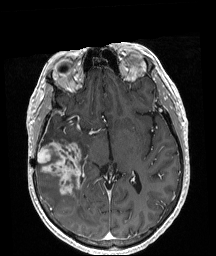
Brain MRI from a brain-tumour surgery series, one axial slice. Slice 109 of 208 in the series (ordered by position). T1-weighted post-contrast. 1 mm slice thickness. 216 × 256 image matrix, field of view 211 × 250 mm. From the clinical record (not read from this slice): histopathology: Astrocytoma; WHO grade: 4; IDH mutation: yes; tumour location: Right Temporal.
Outlined on this slice (expert manual segmentation):
- tumour: bounding box [x1, y1, x2, y2] px = [38, 142, 81, 194]